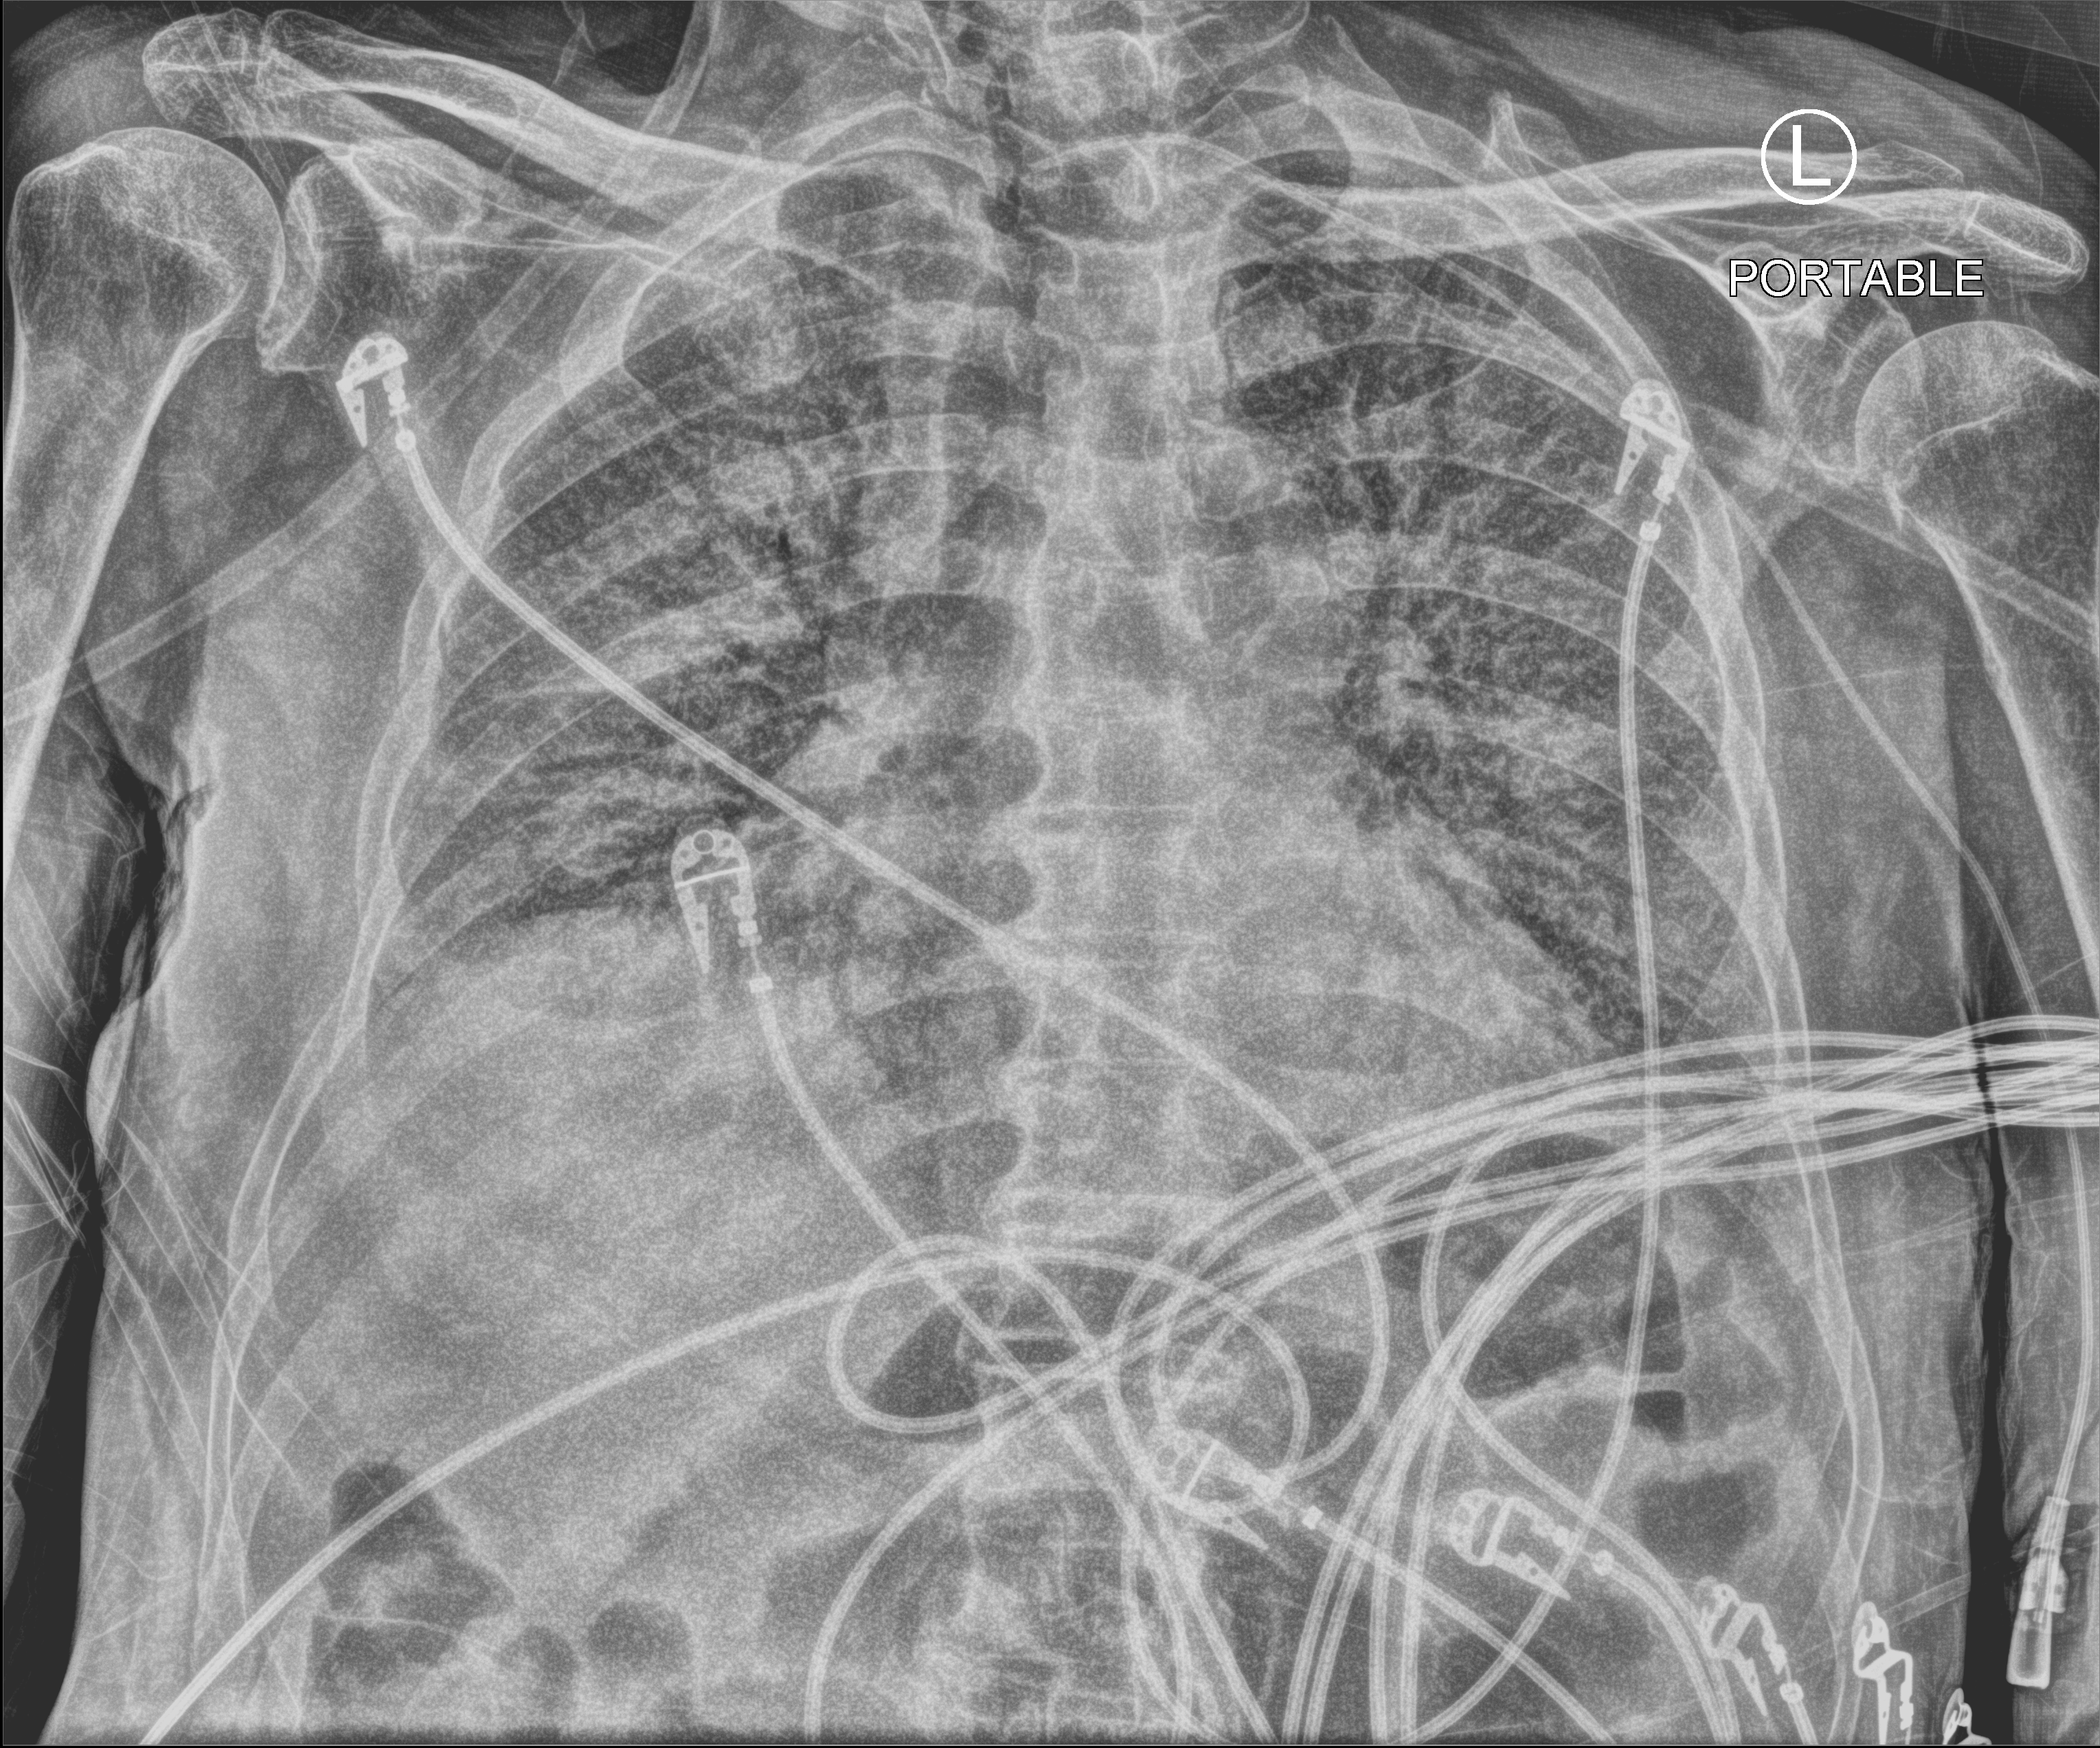
Chest X-ray (portable), anteroposterior (AP) projection. Male patient hospitalised with COVID-19, age 75–90 years.
From the hospital-stay record, not from the radiograph (when in the stay this image was taken is not recorded): length of hospital stay: 30 days; mechanically ventilated during this hospital stay: yes; admitted to intensive care during this hospital stay: yes.